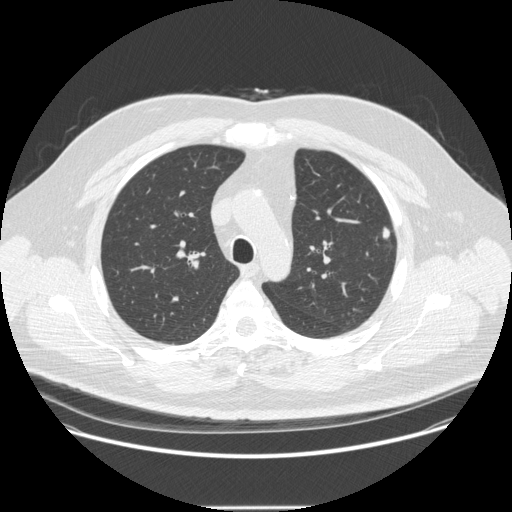
Low-dose screening chest CT, axial slice, second screening round (one year after baseline), lung window (W 1500 / L -600 HU), 1.25 mm slice thickness, standard (soft-tissue) reconstruction kernel (STANDARD), slice 76 of 251 in the series. Male participant, aged 55 years at enrolment. Former smoker at enrolment.
Expert reader's lesion annotation, box from (x=373, y=226) to (x=406, y=250) px. The screening reader recorded 2 non-calcified nodules or masses ≥4 mm on this exam; which of them this box marks is not recorded. Official screen result: positive, other. Lung cancer was diagnosed 60 days after this screen: adenocarcinoma, NOS, left upper lobe, moderately differentiated (G2), stage IA (AJCC 6th edition), 9 mm at pathology.